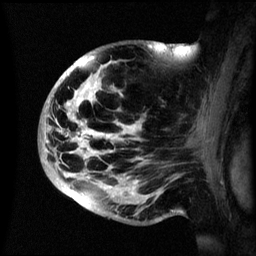
Breast MRI (dynamic contrast-enhanced), one sagittal slice; position 38 of 60 along the scan axis; dynamic contrast-enhanced series, image 2 of 3 at this slice position (ordered by acquisition); 1.5 T; TE 4.2 ms, TR 8.4 ms; 2.4 mm slice thickness; 256 × 256 image matrix, field of view 230 × 230 mm. Patient: female, 48 years.
Structures marked on this image (semi-automatically segmented with operator editing):
- analysis volume of interest (the breast-tissue region the enhancement analysis was run in; not a lesion): bounding box (x1, y1, x2, y2) in pixels: (40, 42, 195, 222)
- tumour enhancement mask (voxels above the 70 % enhancement threshold inside the analysis volume of interest): (45, 43, 156, 199)